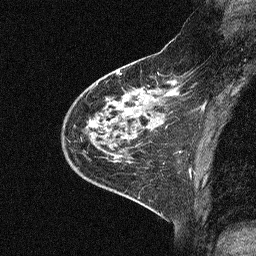
Breast MRI (dynamic contrast-enhanced), one sagittal slice; position 19 of 64 along the scan axis; dynamic contrast-enhanced study with each time point stored as its own series, time point 2 of 3 at this slice position (early post-contrast, ordered by acquisition time); 1.5 T; TE 4.5 ms, TR 11 ms; 2.06 mm slice thickness; 256 × 256 image matrix, field of view 200 × 200 mm. Female patient, age 46 years. From the clinical record (not read from this slice): setting: breast cancer imaged before/during neoadjuvant chemotherapy; receptor status: HER2-positive.
Structures marked on this image (semi-automatically segmented with operator editing):
- analysis volume of interest (the breast-tissue region the enhancement analysis was run in; not a lesion): bounding box (x1, y1, x2, y2) in pixels: (47, 51, 180, 169)
- tumour enhancement mask (voxels above the 90 % enhancement threshold inside the analysis volume of interest): (89, 98, 119, 119)